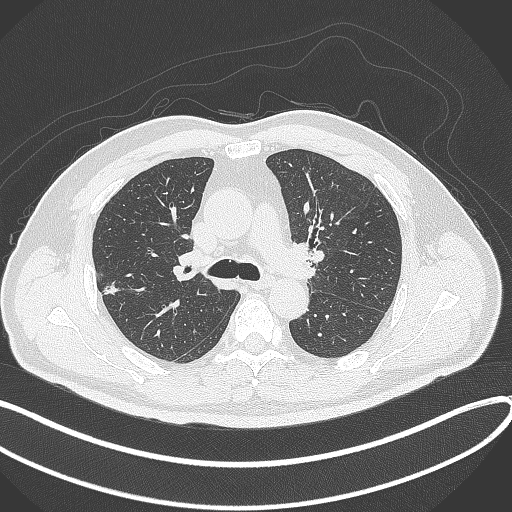
Chest CT, one axial slice. Position 222 of 372 along the scan axis. Reconstruction kernel B70f. 120 kVp. Lung window (W 1500 / L -600 HU). 1 mm slice thickness. 512 × 512 image matrix, field of view 400 × 400 mm. Patient: male, 60 years. From the clinical record (not read from this slice): clinical TNM (as recorded): T1c N0 M0.
Annotated regions visible in this slice (rectangle marked by the reading radiologist):
- lung tumour (recorded histology: adenocarcinoma): bounding box (x1, y1, x2, y2) in pixels: (99, 281, 123, 299)